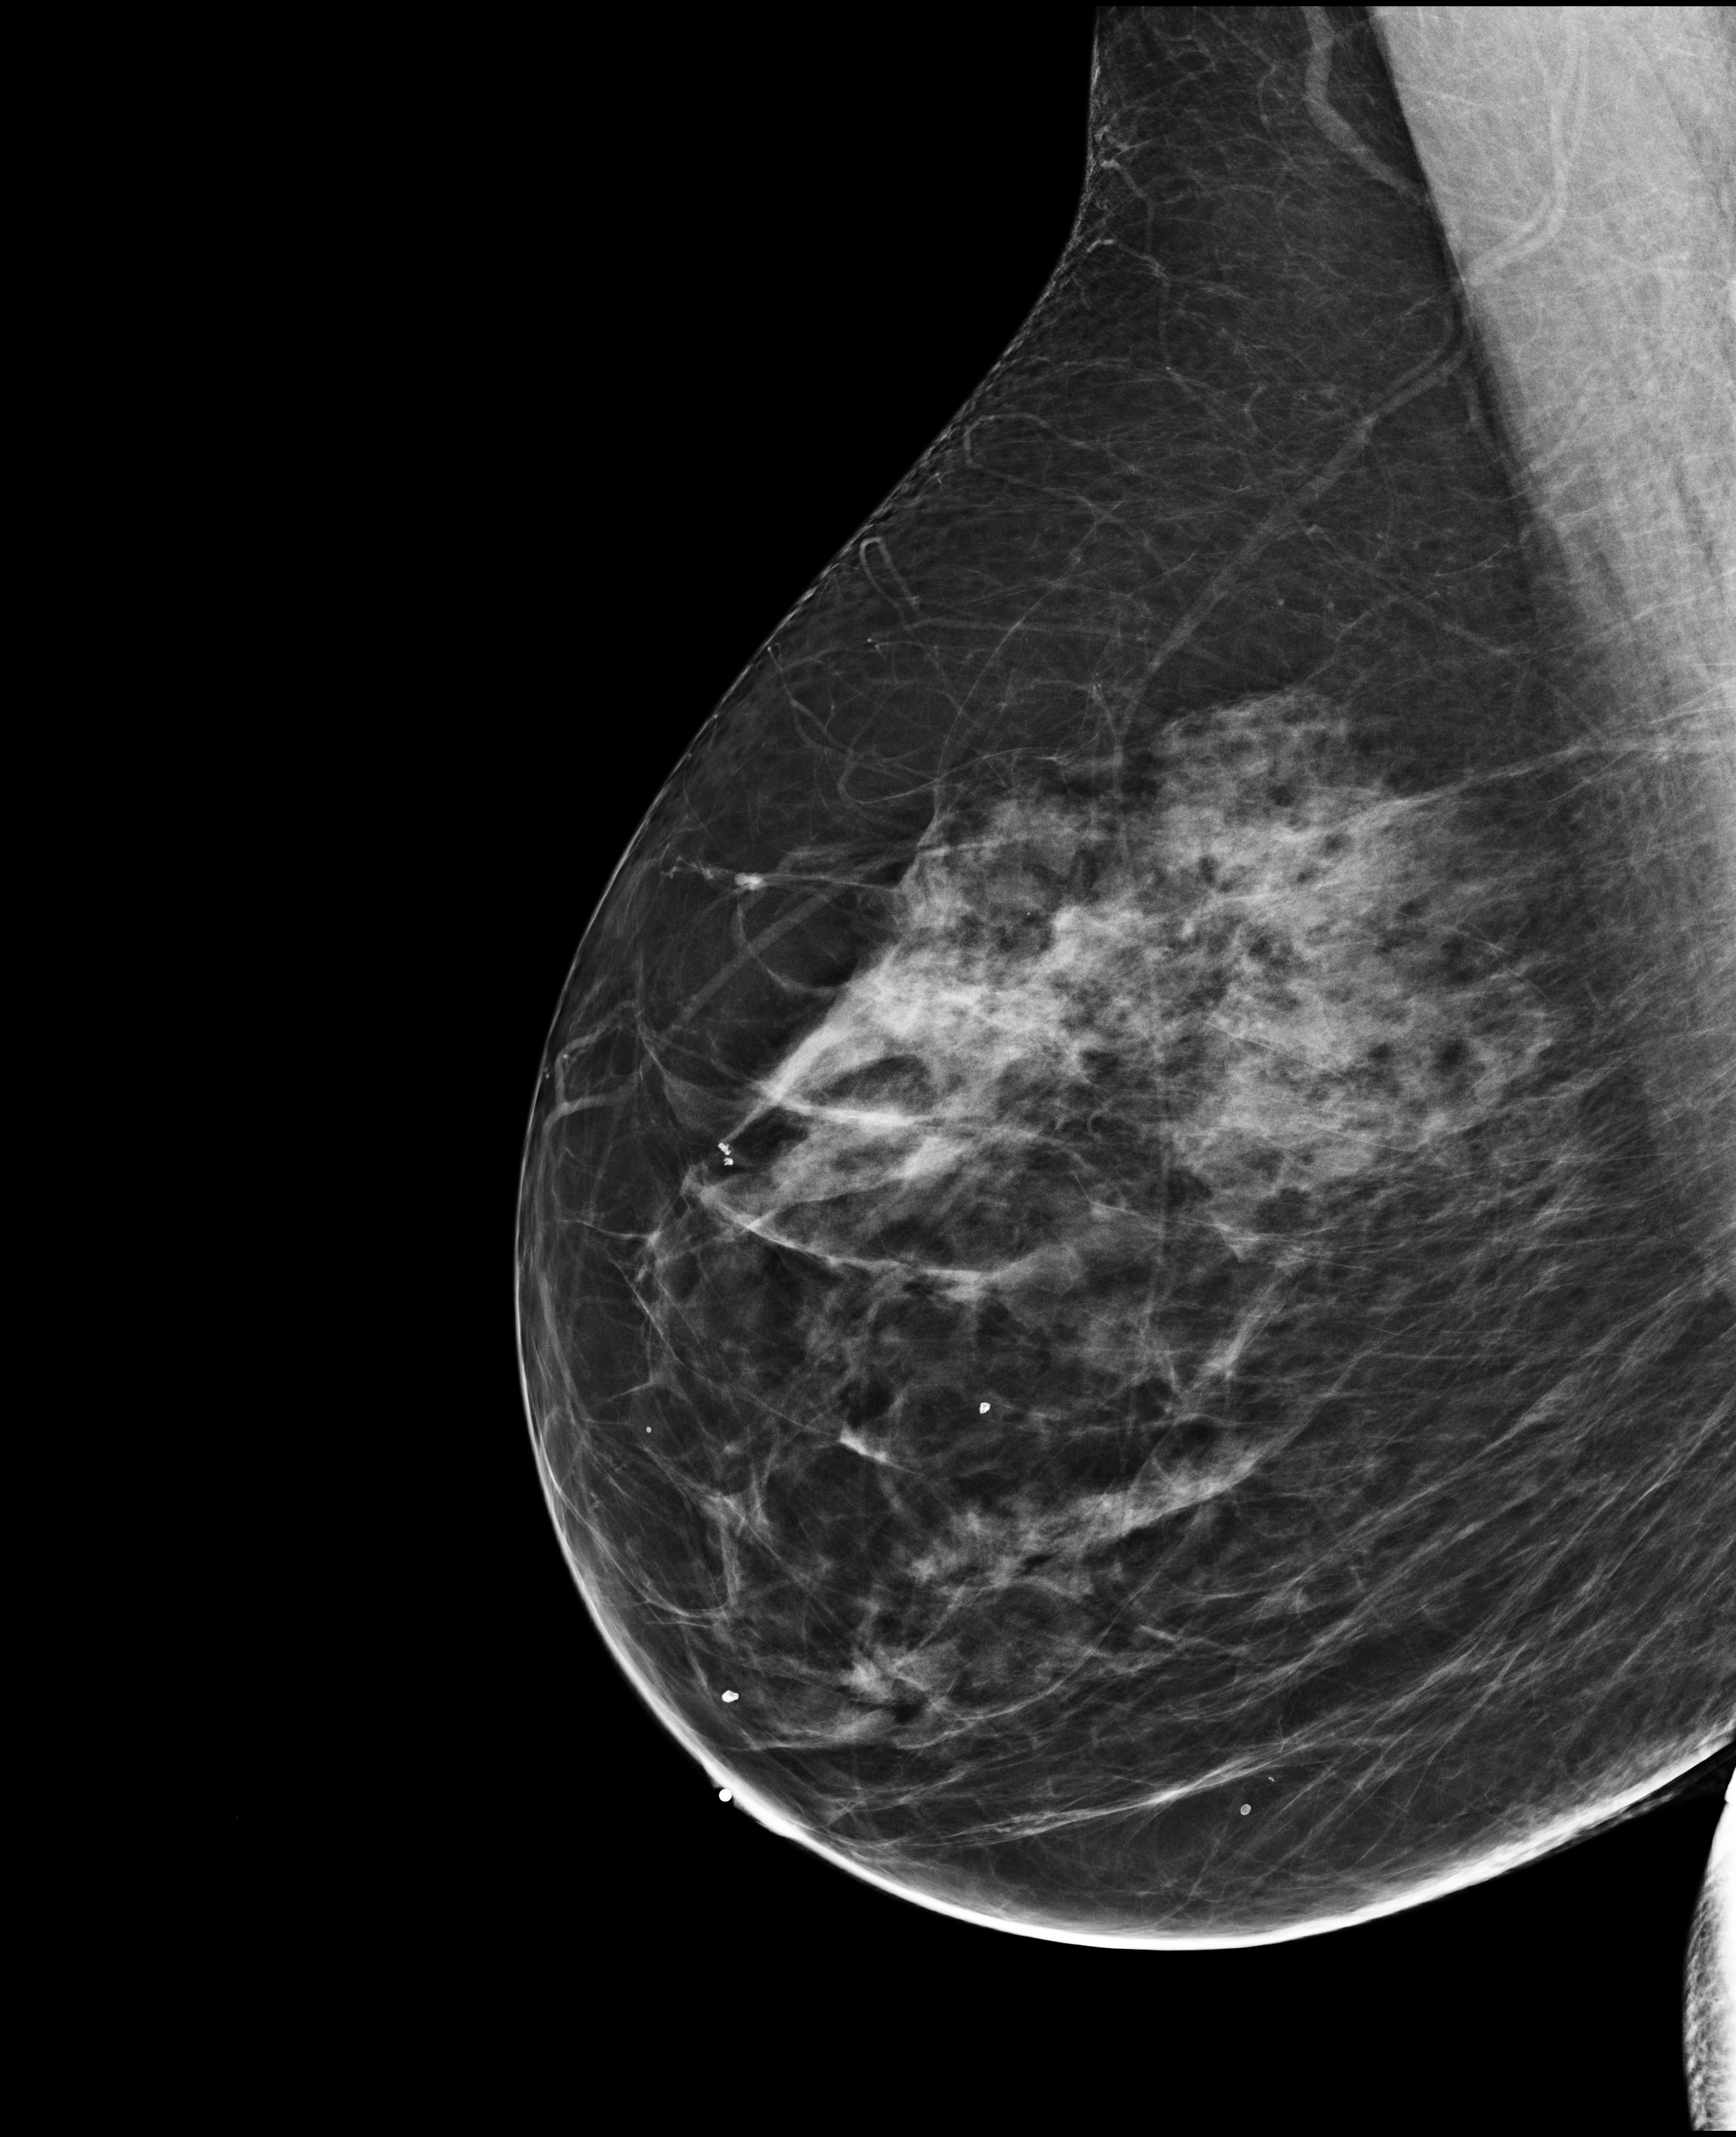
Full-field digital mammogram (FFDM); right breast; medio-lateral oblique projection; annual screening mammography examination; compressed breast thickness 79 mm. Patient aged 60 years (female).
Breast density at the screening exam (both breasts): heterogeneously dense (BI-RADS density category c). Final BI-RADS assessment for this screening round (tomosynthesis exam, both breasts): category 1. Recall: no recall after this screen.